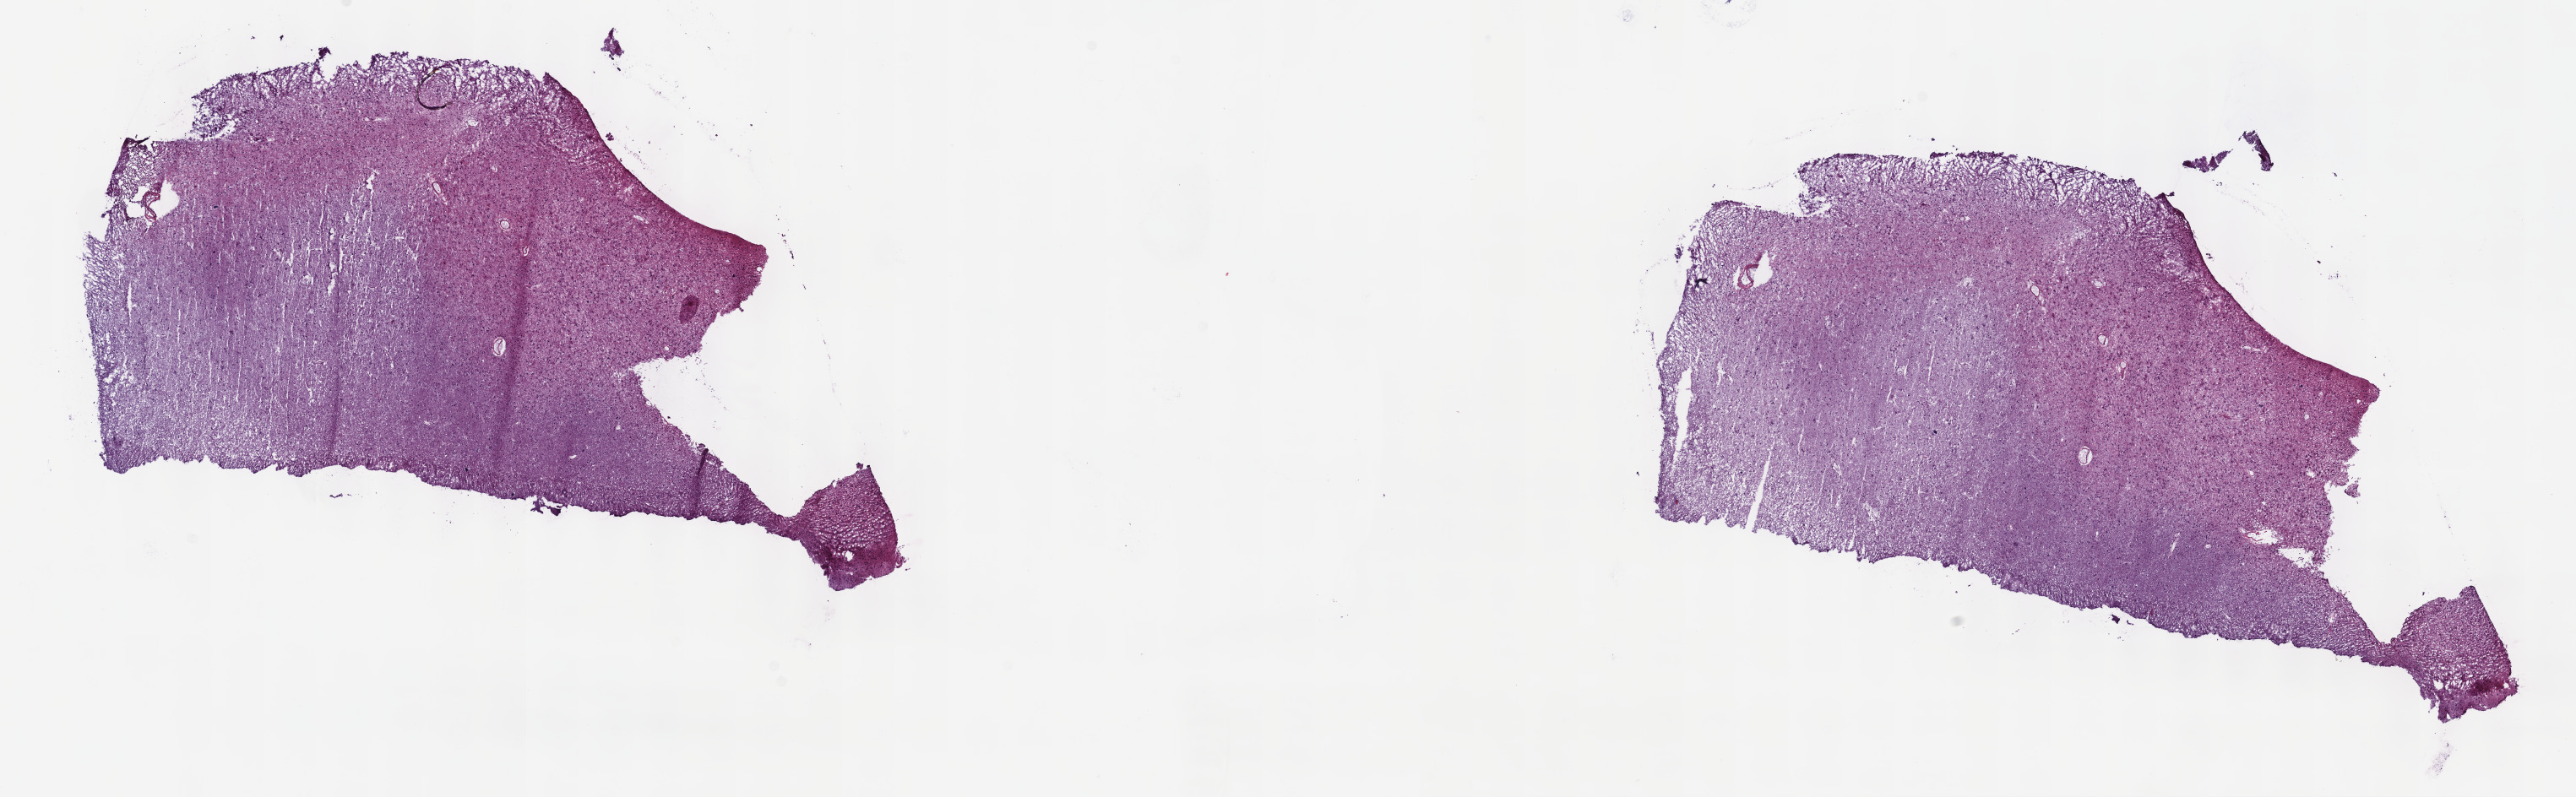
H&E-stained whole-slide image — low-resolution overview of the scanned area, about 24.7 x 7.6 mm (slide scanned at 40x); frozen section; recurrent tumour sample from the brain. Male patient; age at initial diagnosis 27 years. Pathologist review of this section (percent, as recorded): tumour cells 30%, tumour nuclei 70%.
This section: recurrent tumour. Patient diagnosis: Mixed glioma (cerebrum).